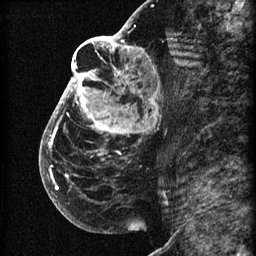
Breast MRI (dynamic contrast-enhanced), one sagittal slice. Position 36 of 60 along the scan axis. 3 images stored at this slice position (order not interpretable as contrast timing). 1.5 T. TE 4.2 ms, TR 22.7 ms. 2 mm slice thickness. 256 × 256 image matrix, field of view 180 × 180 mm. Female patient, age 48 years. From the clinical record (not read from this slice): setting: breast cancer imaged before/during neoadjuvant chemotherapy; receptor status: triple-negative.
Annotated regions visible in this slice (semi-automatic segmentation, software-assisted and operator-edited):
- analysis volume of interest (the breast-tissue region the enhancement analysis was run in; not a lesion): bounding box (x1, y1, x2, y2) in pixels: (44, 30, 173, 207)
- tumour enhancement mask (voxels above the 90 % enhancement threshold inside the analysis volume of interest): (44, 30, 154, 190)